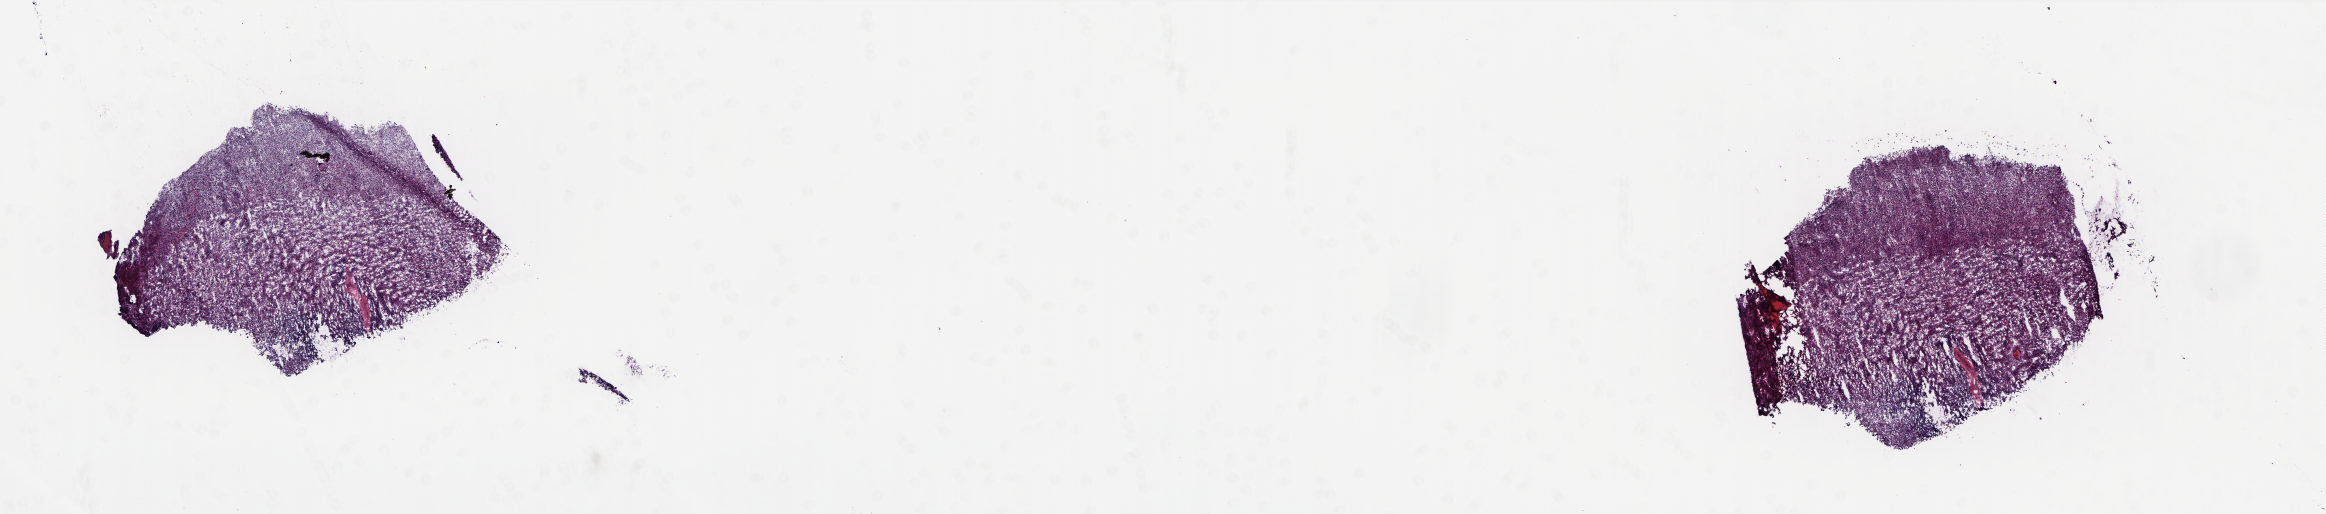
Digitized H&E tissue section (whole slide), low-resolution overview of the scanned area, about 18.8 x 4.1 mm; frozen section; adrenal cortex, solid tissue normal (non-tumour tissue) sample. Male patient; age at initial diagnosis 63 years. Composition of this section per pathologist review: tumour cells 0%, tumour nuclei 0%, normal cells 100%, stromal cells 0%, necrosis 0%. Inflammatory infiltration, as recorded: lymphocyte infiltration 1%, monocyte infiltration 0%, neutrophil infiltration 0%.
This section: solid tissue normal (non-tumour) sample from the same patient. Patient diagnosis: Adrenal cortical carcinoma (cortex of adrenal gland).